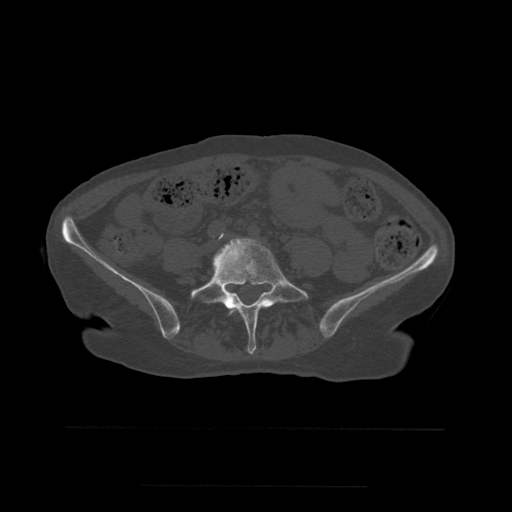
CT including the spine, one axial slice; position 148 of 544 along the scan axis; bone window (W 1800 / L 400 HU); 1.25 mm slice thickness; 512 × 512 image matrix, field of view 350 × 350 mm. Patient age 58 years. Case-level facts recorded for this patient, not image findings: primary cancer: lung.
Outlined on this slice (semi-automatically segmented with operator editing):
- L4 vertebra: bounding box [x1, y1, x2, y2] px = [229, 309, 236, 316]
- L5 vertebra: [191, 238, 302, 354]